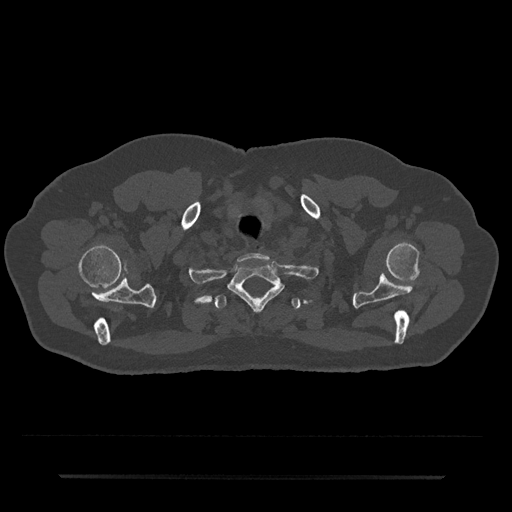
CT including the spine, one axial slice. Slice 636 of 797 in the series (ordered by position). Bone window (W 1800 / L 400 HU). 0.5 mm slice thickness. 512 × 512 image matrix, field of view 437 × 437 mm. Male patient, age 69 years. Case-level facts recorded for this patient, not image findings: primary cancer: prostate.
Annotated regions visible in this slice (semi-automatically segmented with operator editing):
- T1 vertebra: box from (x=229, y=262) to (x=283, y=311) px
- T2 vertebra: (x=214, y=295)–(x=301, y=309)